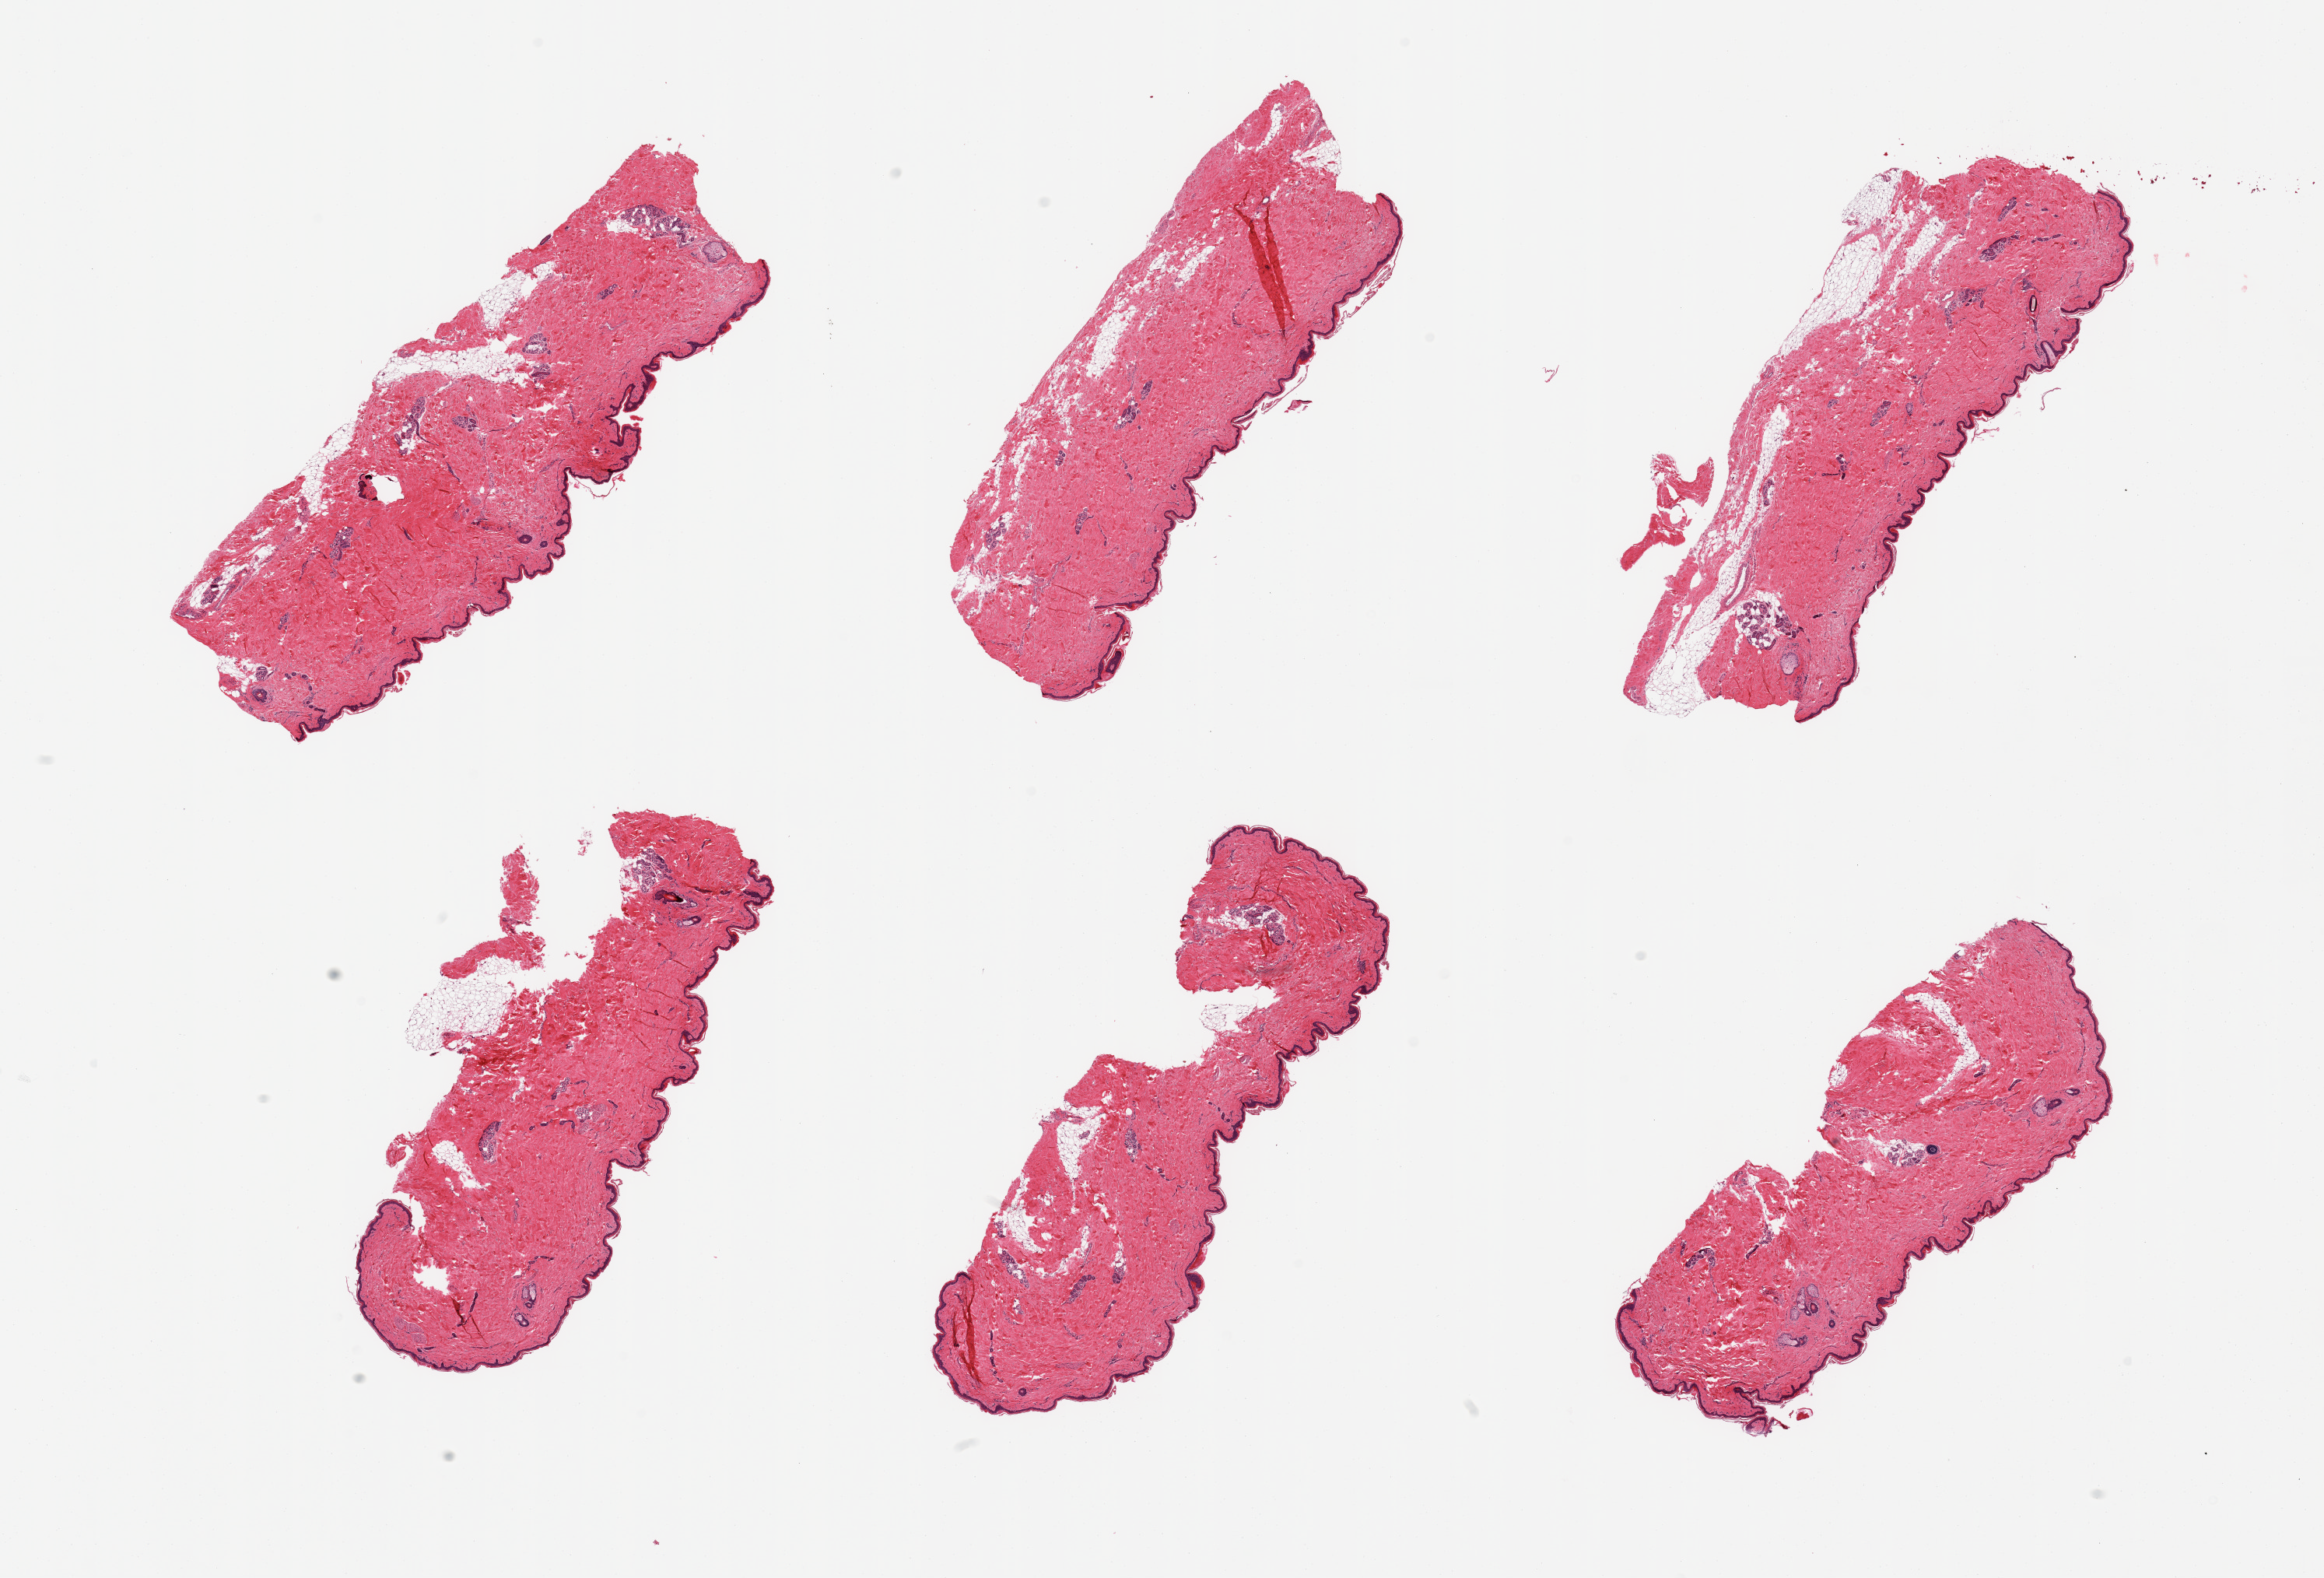
Whole-slide image, haematoxylin and eosin stain, brightfield, whole scanned area (about 23.6 x 16.0 mm, from a 20x scan) shown as a low-resolution overview, PAXgene-fixed paraffin-embedded (PFPE) section, target tissue: skin of suprapubic region, donor tissue sample. Female donor.
• reviewer comment on this tissue sample: 6 pieces; 10% dermal fat; well trimmed